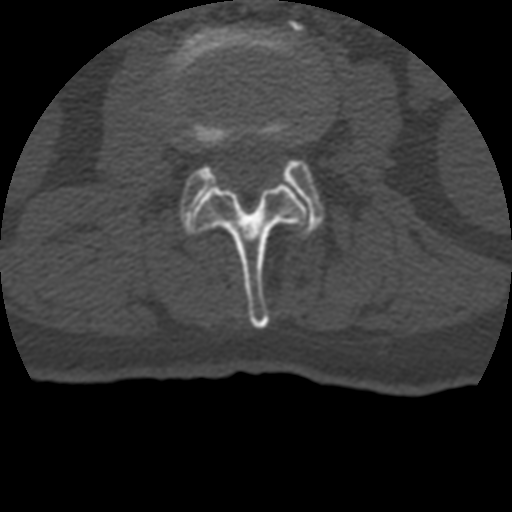
CT including the spine, one axial slice. Slice 104 of 399 in the series (ordered by position). Reconstruction kernel STANDARD. 120 kVp. Bone window (W 1800 / L 400 HU). 512 × 512 image matrix. Patient age 69 years. From the clinical record (not read from this slice): primary cancer: prostate.
Structures marked on this image (semi-automatically segmented with operator editing):
- L2 vertebra: bounding box (x1, y1, x2, y2) in pixels: (195, 185, 306, 329)
- L3 vertebra: (163, 23, 324, 228)